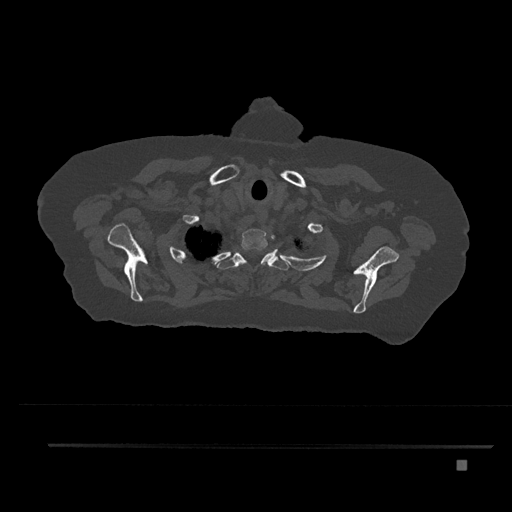
CT including the spine, one axial slice. Position 681 of 797 along the scan axis. Bone window (W 1800 / L 400 HU). 0.5 mm slice thickness. 512 × 512 image matrix, field of view 437 × 437 mm. Female patient, age 76 years. Case-level facts recorded for this patient, not image findings: primary cancer: lung; vertebrae with lytic lesions (as recorded): T11, L3.
Structures marked on this image (semi-automatic segmentation, software-assisted and operator-edited):
- T1 vertebra: bounding box [x1, y1, x2, y2] px = [241, 229, 277, 262]
- T2 vertebra: [217, 250, 289, 270]